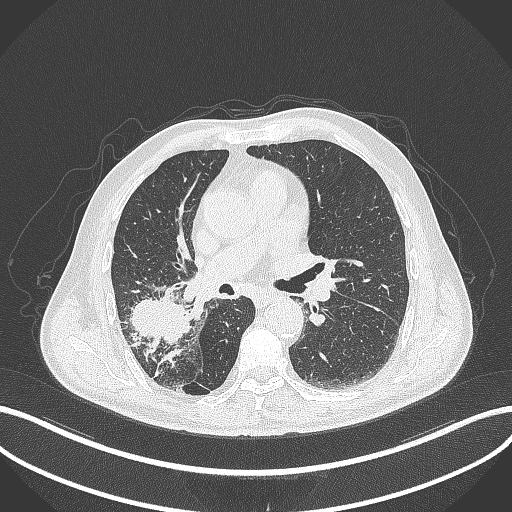
Chest CT, one axial slice; position 231 of 429 along the scan axis; reconstruction kernel B70f; lung window (W 1500 / L -600 HU); 1 mm slice thickness; 512 × 512 image matrix, field of view 400 × 400 mm. Patient: male, 72 years. From the clinical record (not read from this slice): clinical TNM (as recorded): T3 N2 M0.
Annotated regions visible in this slice (rectangle marked by the reading radiologist):
- lung tumour (recorded histology: adenocarcinoma): bounding box <125,287,189,346> (left, top, right, bottom; pixels)